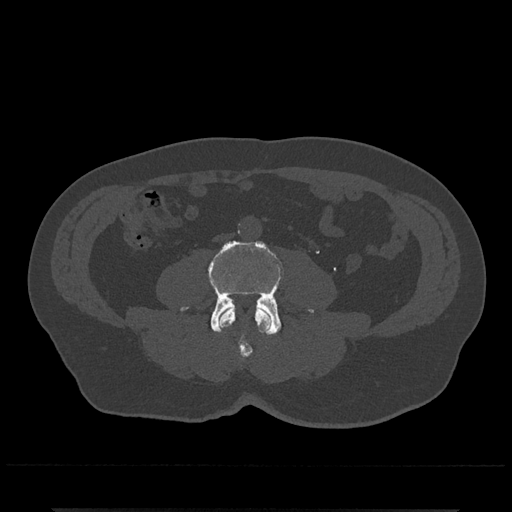
CT including the spine, one axial slice. Position 178 of 797 along the scan axis. Reconstruction kernel Br40s/3. Bone window (W 1800 / L 400 HU). 512 × 512 image matrix, field of view 393 × 393 mm. Male patient, age 67 years. From the clinical record (not read from this slice): primary cancer: prostate.
Annotated regions visible in this slice (semi-automatically segmented with operator editing):
- L3 vertebra: bounding box <219,307,272,358> (left, top, right, bottom; pixels)
- L4 vertebra: <181,241,313,335>